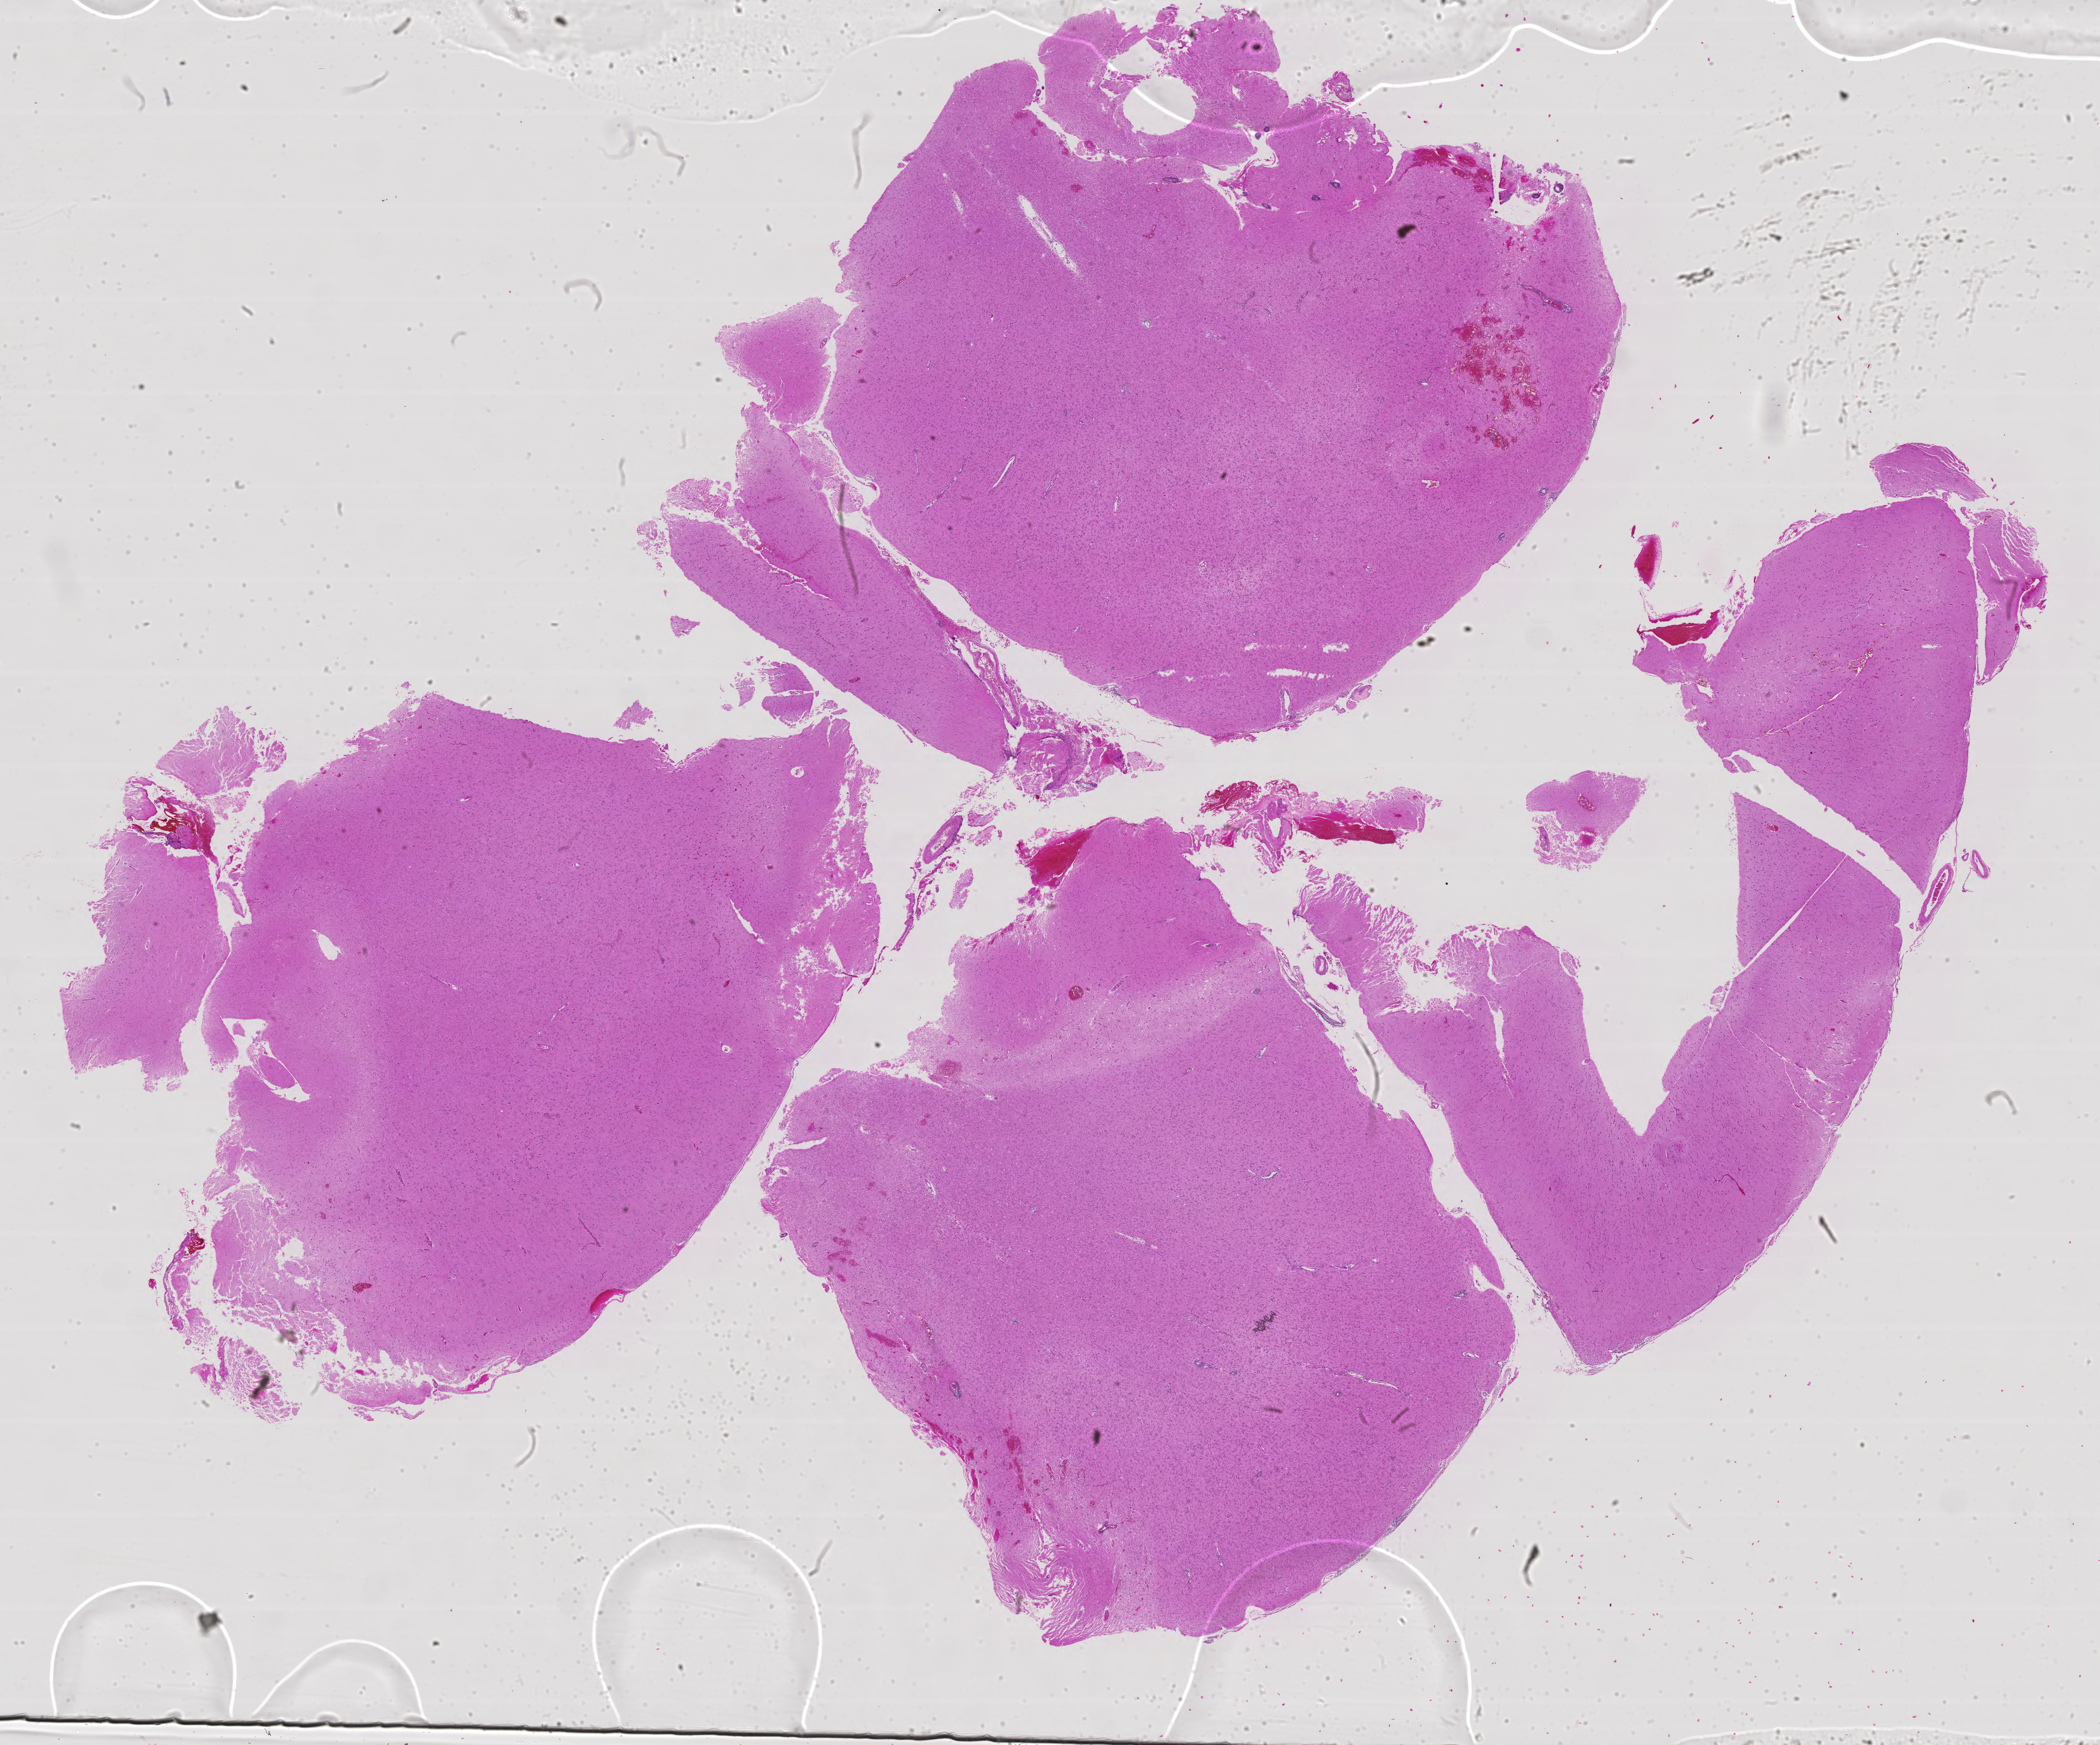
Whole-slide histology image, H&E-stained — a low-resolution overview of the entire scanned area, about 28.3 x 23.5 mm (from a 40x scan). Formalin-fixed paraffin-embedded (FFPE) diagnostic section. Brain, primary tumour sample. Patient: female, age at initial diagnosis 63 years. Histologic grade: G3 (poorly differentiated).
Pathologic diagnosis: Astrocytoma, anaplastic (cerebrum).